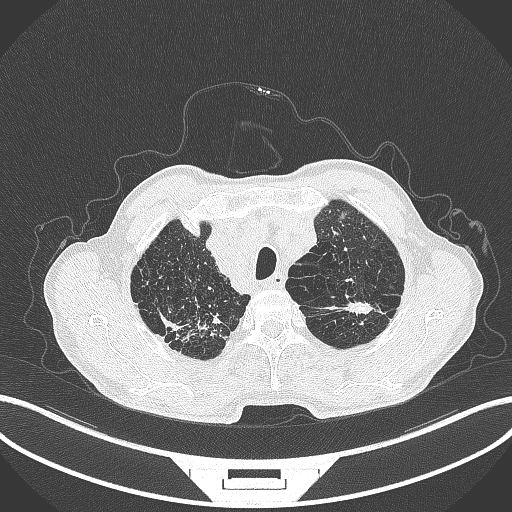
Chest CT, one axial slice; slice 381 of 463 in the series (ordered by position); 120 kVp; lung window (W 1500 / L -600 HU); 1 mm slice thickness; 512 × 512 image matrix. Patient: male, 74 years. From the clinical record (not read from this slice): clinical TNM (as recorded): T2a N1 M0.
Outlined on this slice (rectangle marked by the reading radiologist):
- lung tumour (recorded histology: adenocarcinoma): box from (x=333, y=298) to (x=374, y=317) px